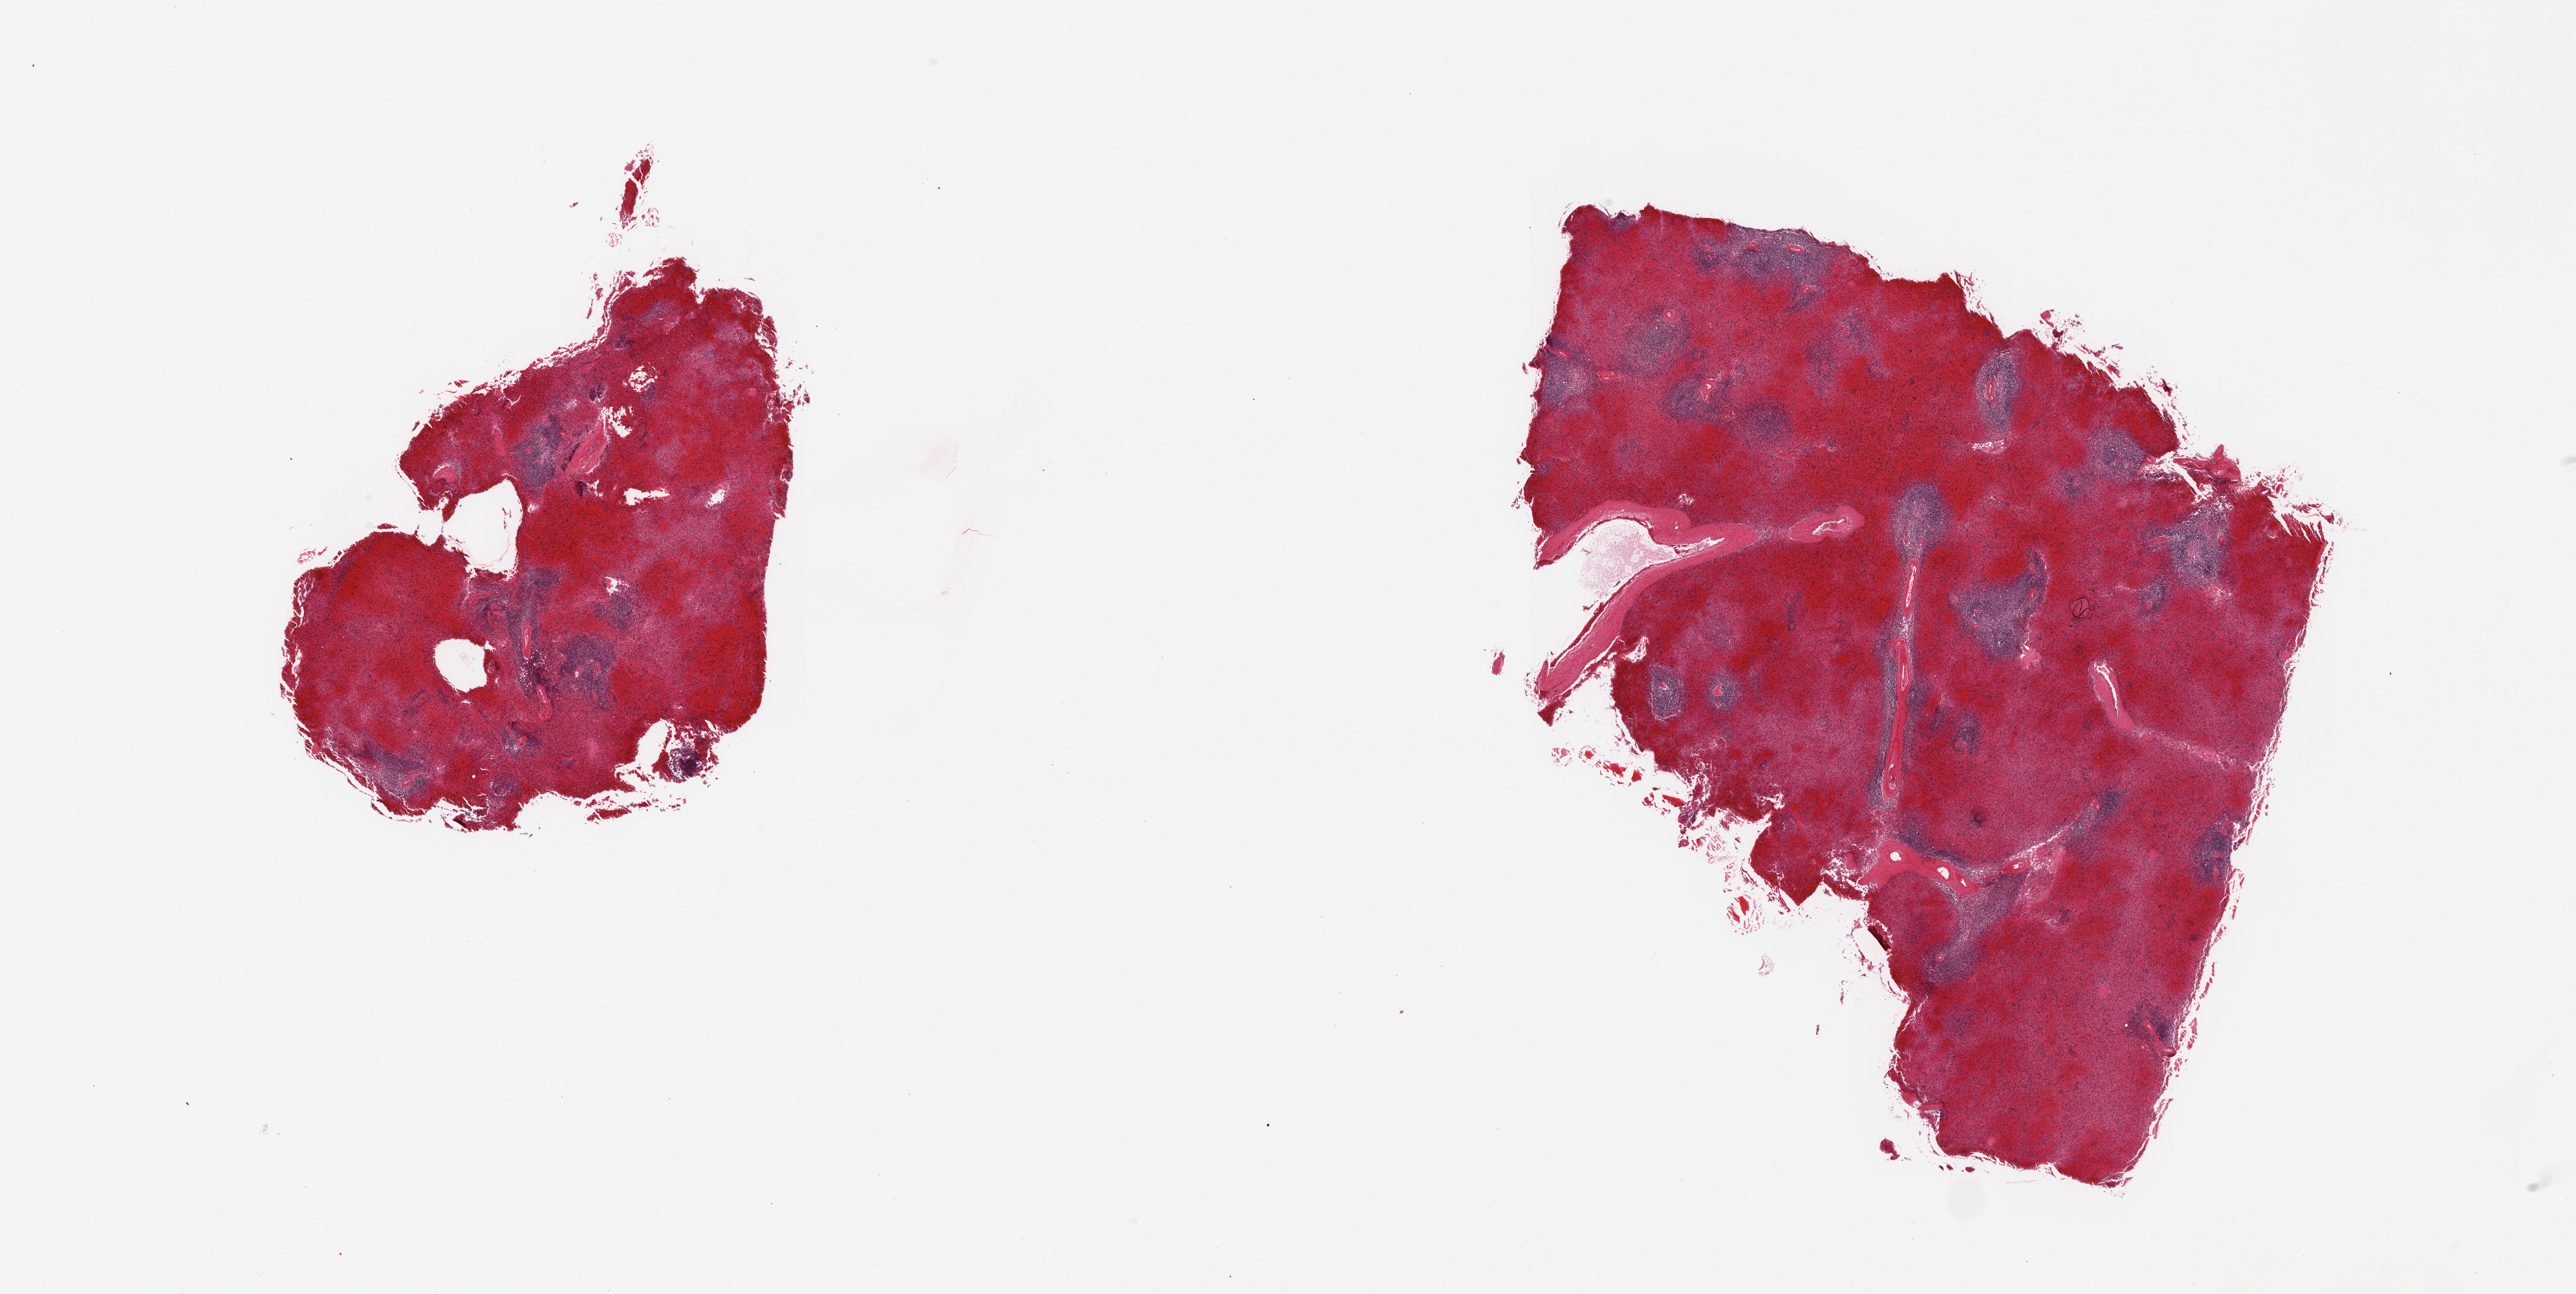
Haematoxylin and eosin whole-slide image, a low-resolution overview of the entire scanned area, about 31.5 x 15.8 mm (slide scanned at 20x). PAXgene-fixed paraffin-embedded (PFPE) section. Target tissue: spleen. Tissue donor sample. Male donor.
Review note (as recorded): 2 pieces; marked congestion.